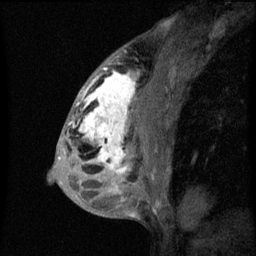
Breast MRI (dynamic contrast-enhanced), one sagittal slice. Slice 33 of 60 in the series (ordered by position). Dynamic contrast-enhanced series, image 2 of 3 at this slice position (ordered by acquisition). 1.5 T. TE 4.2 ms, TR 8 ms. 2 mm slice thickness. 256 × 256 image matrix, field of view 180 × 180 mm. Patient: female, 50 years.
Structures marked on this image (semi-automatic segmentation, software-assisted and operator-edited):
- analysis volume of interest (the breast-tissue region the enhancement analysis was run in; not a lesion): bounding box [x1, y1, x2, y2] px = [66, 64, 141, 187]
- tumour enhancement mask (voxels above the 70 % enhancement threshold inside the analysis volume of interest): [69, 68, 136, 175]